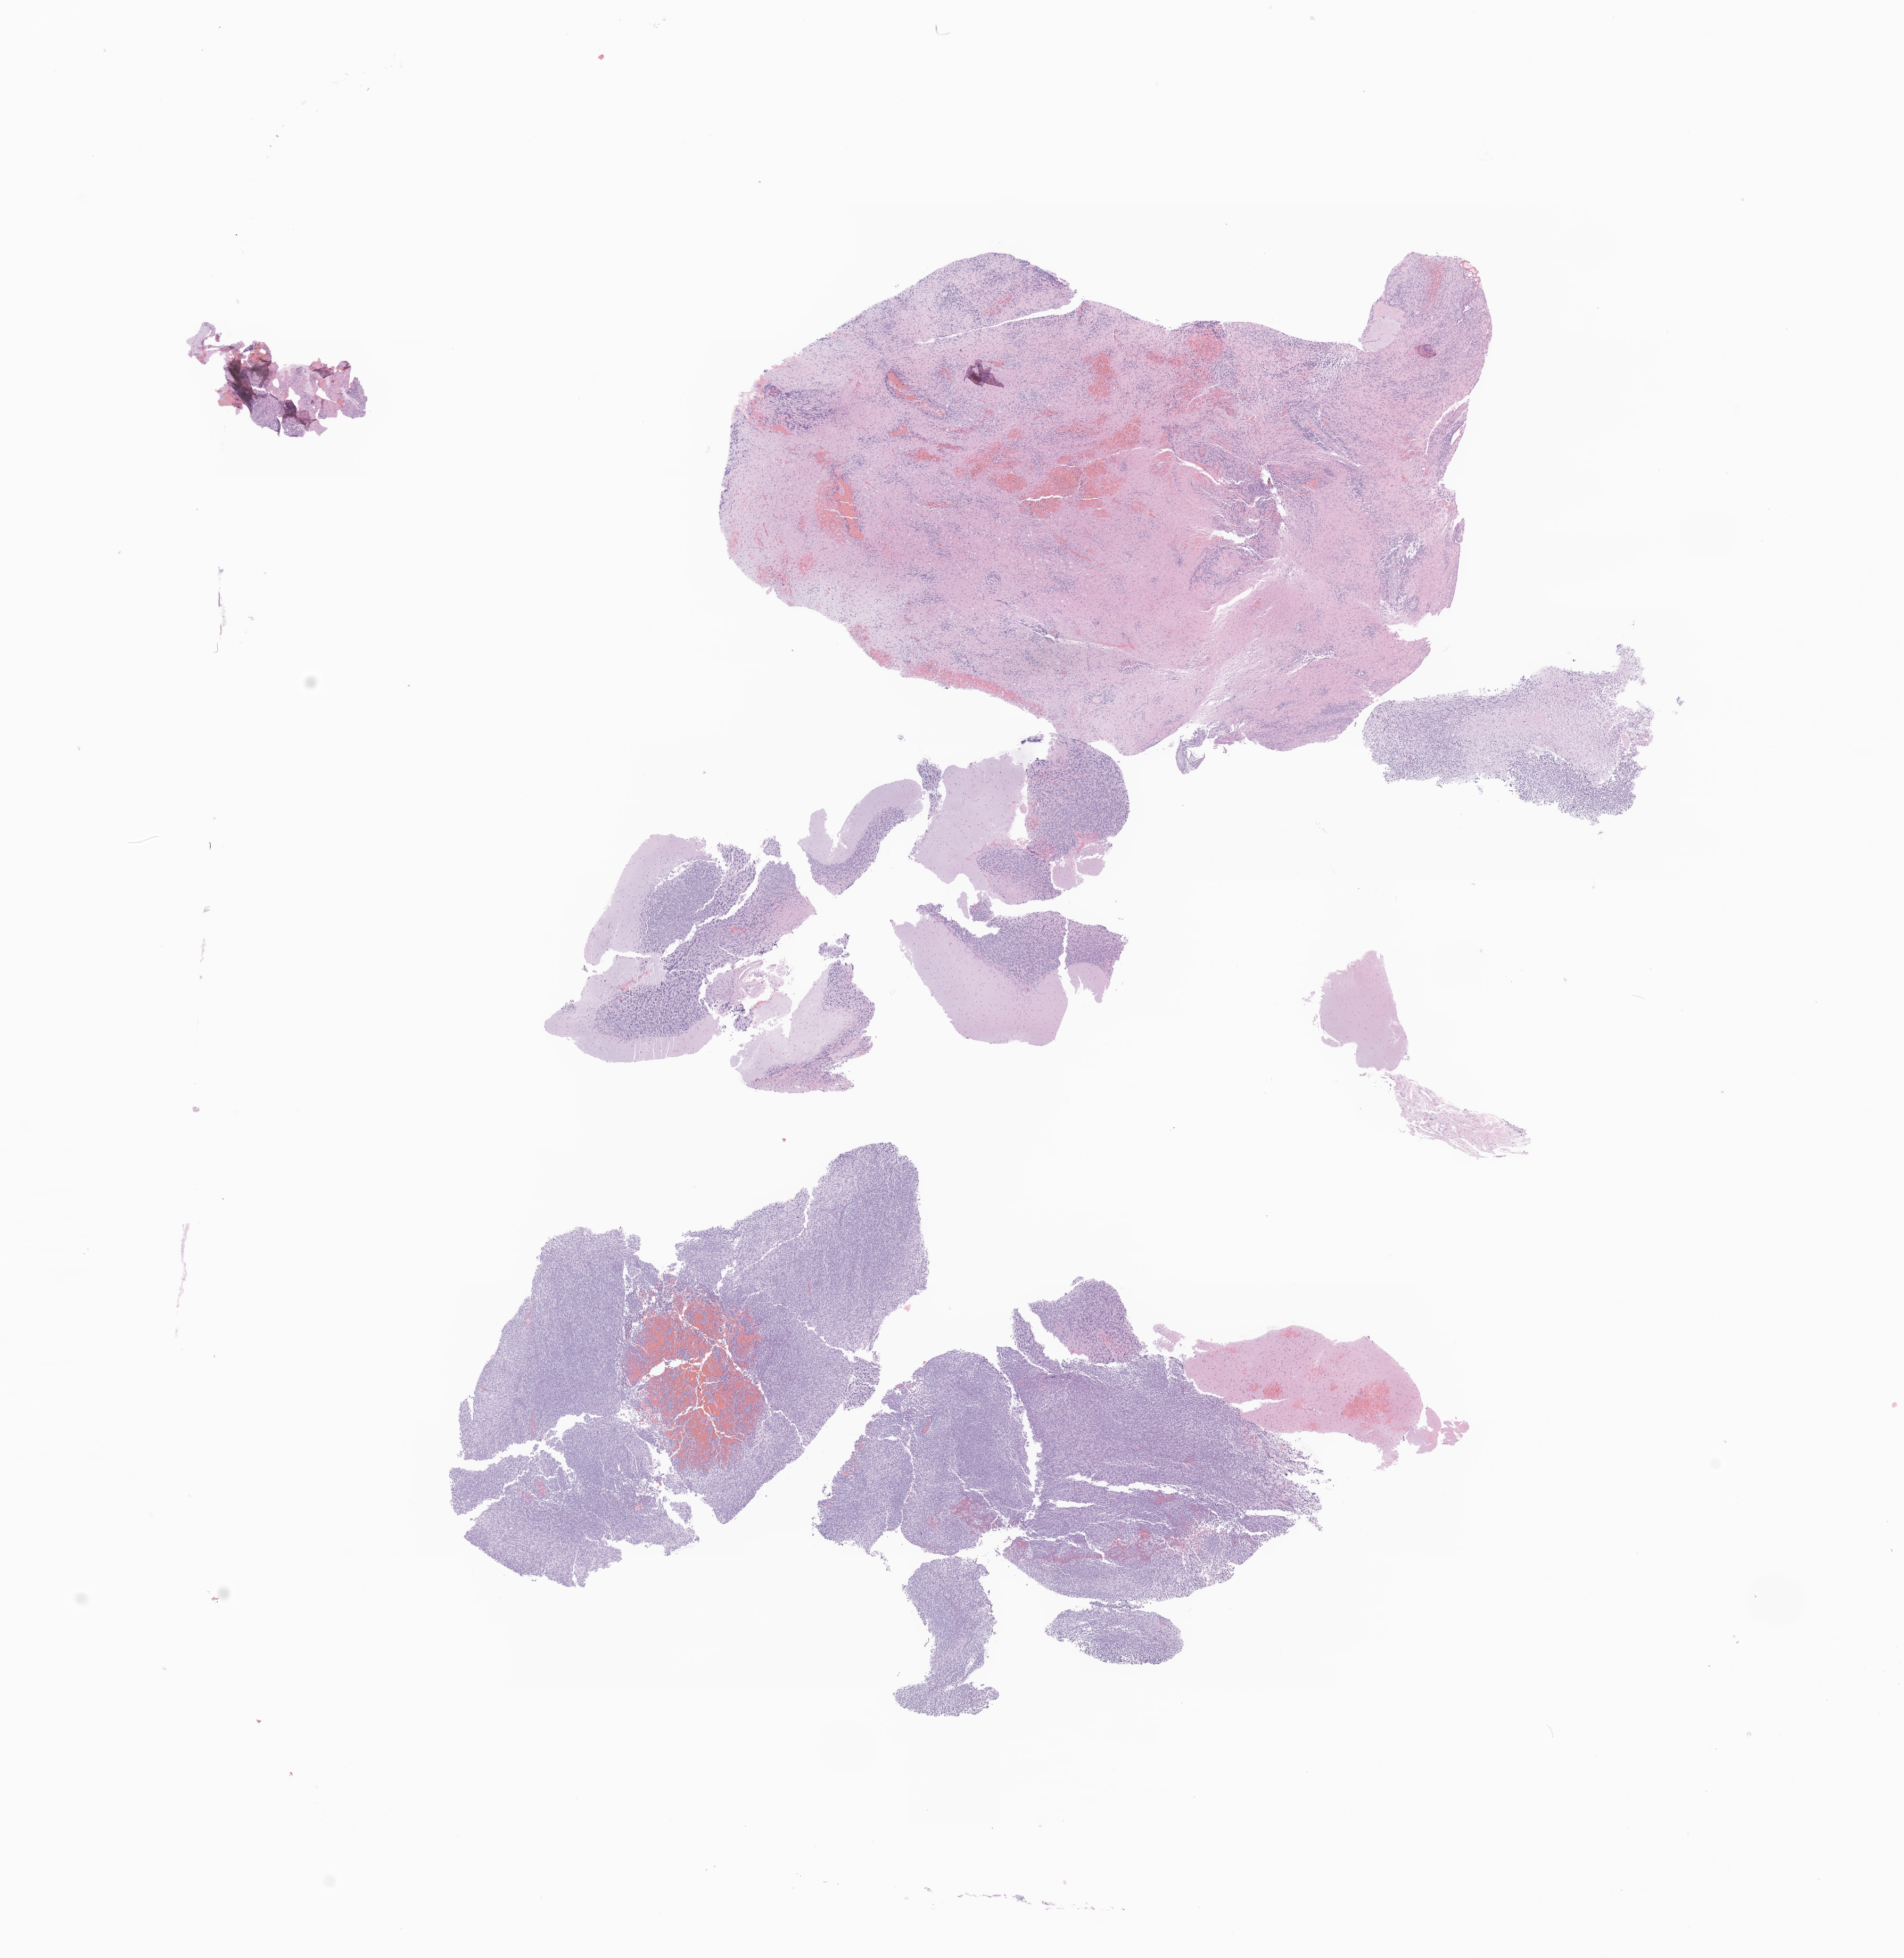
H&E whole-slide image of tumor tissue from the brain — low-resolution overview of the scanned area, about 15.1 x 15.5 mm; FFPE section. Patient: male, age 225 months (18 years 9 months).
• diagnosis (ICD-O-3 morphology term): Medulloblastoma, NOS